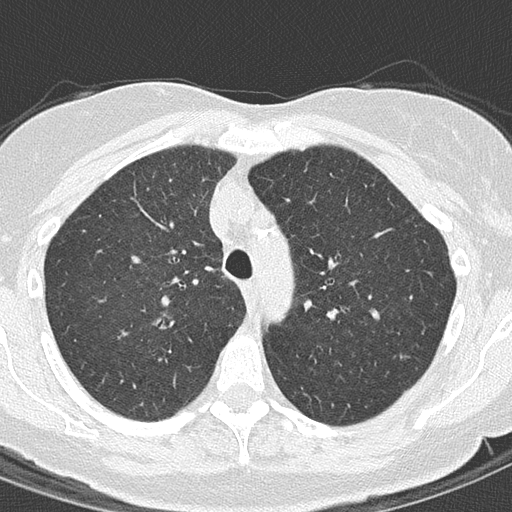
Low-dose screening chest CT, axial slice, second annual screen, lung window (W 1500 / L -600 HU), lung (sharp) reconstruction kernel (B50f), 512 × 512 image matrix. Female, age 61 years at enrolment.
Expert-annotated lung lesion, bounding box [x1, y1, x2, y2] px = [146, 301, 189, 339]. The exam's reader record, not a measurement of the box and not confirmed to be the same lesion: non-calcified nodule or mass ≥4 mm, right upper lobe, 15 × 10 mm, spiculated (stellate) margins, ground glass attenuation, pre-existing on the prior screen: yes; interval growth: yes. Official screen result: positive, other. Participant outcome: lung cancer diagnosed 91 days after this screen — adenocarcinoma, NOS, right upper lobe, moderately differentiated (G2), stage IA (AJCC 6th edition), 20 mm at pathology.